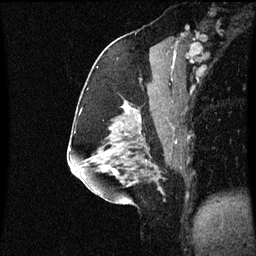
Breast MRI (dynamic contrast-enhanced), one sagittal slice. Position 29 of 60 along the scan axis. Dynamic contrast-enhanced series, image 2 of 3 at this slice position (ordered by acquisition). 1.5 T. TE 4.2 ms, TR 8.9 ms. 2 mm slice thickness. 256 × 256 image matrix, field of view 200 × 200 mm. Female patient, age 58 years. Case-level facts recorded for this patient, not image findings: setting: breast cancer imaged before/during neoadjuvant chemotherapy; receptor status: triple-negative.
Outlined on this slice (semi-automatically segmented with operator editing):
- analysis volume of interest (the breast-tissue region the enhancement analysis was run in; not a lesion): bounding box <104,118,171,179> (left, top, right, bottom; pixels)
- tumour enhancement mask (voxels above the 70 % enhancement threshold inside the analysis volume of interest): <114,118,141,175>